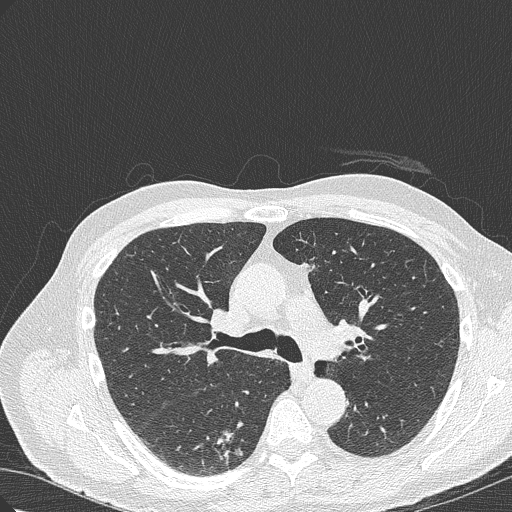
Axial slice from a low-dose chest CT screening exam; first (baseline) screen; lung window (W 1500 / L -600 HU); 1 mm slice thickness; lung (sharp) reconstruction kernel (B50f); slice 114 of 322 in the series; 512 × 512 image matrix. Male participant, aged 70 years at enrolment. Current smoker at enrolment.
• Lesion marked by an expert reader, bounding box [x1, y1, x2, y2] px = [201, 419, 265, 467].
• The screening reader recorded 4 non-calcified nodules or masses ≥4 mm on this exam (right lower lobe, right lower lobe, right upper lobe, right lower lobe); which of them this box marks is not recorded.
• Lung cancer was diagnosed 978 days after this screen (after the third annual screen): bronchiolo-alveolar adenocarcinoma, NOS, right lower lobe, poorly differentiated (G3), stage IB (AJCC 6th edition), 30 mm at pathology.